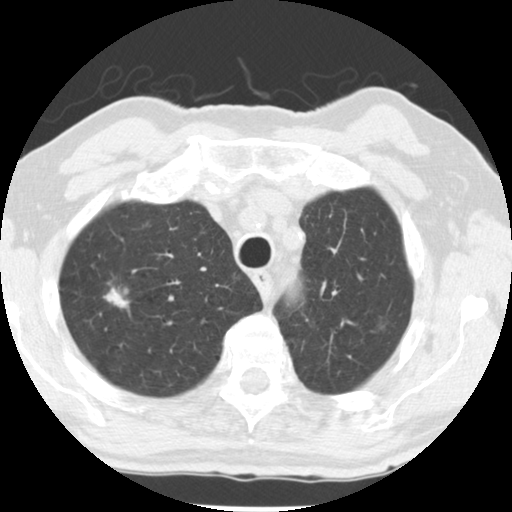
Low-dose screening chest CT, one axial slice; 120 kVp; lung window (W 1500 / L -600 HU); 2.5 mm slice thickness; 512 × 512 image matrix.
Outlined on this slice (expert manual segmentation):
- lesion 1 (tumor, upper lobe of right lung): bounding box [x1, y1, x2, y2] px = [104, 287, 130, 310]